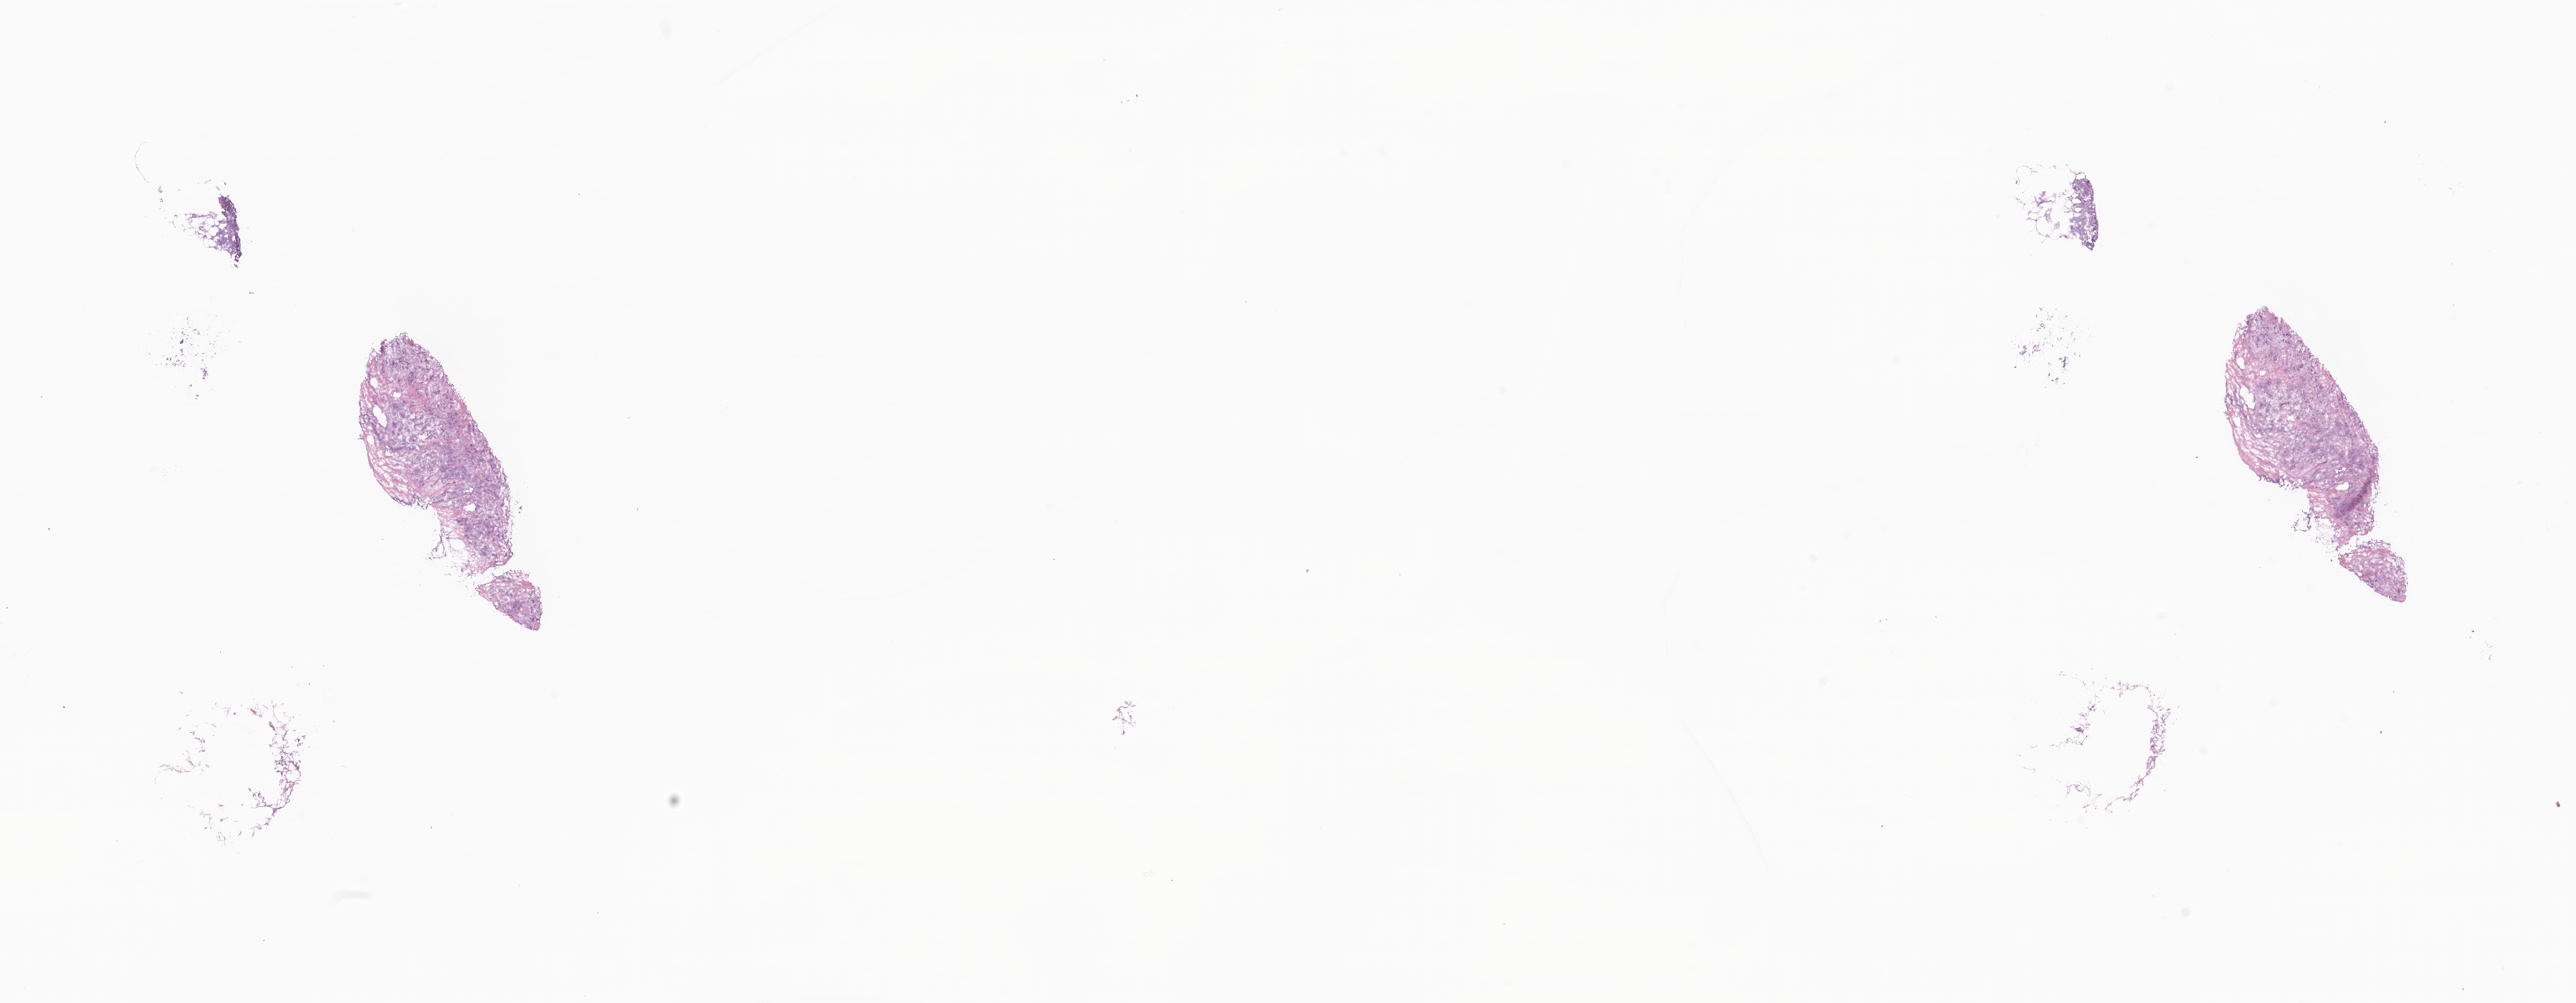
Whole-slide image, hematoxylin and eosin (H&E) stain, a low-resolution overview of the entire scanned area, about 28.2 x 11.0 mm, frozen section, specimen: primary tumor, site: breast. Female patient; age at initial diagnosis 76 years. Pathologist review of this section (percent, as recorded): tumor cells 75%, tumor nuclei 87%, stromal cells 20%, necrosis 5%, normal cells 0%. Inflammatory infiltration, as recorded: lymphocyte infiltration 0%, monocyte infiltration 0%, neutrophil infiltration 0%.
* section: top of the tissue portion
* diagnosis: Infiltrating duct carcinoma, NOS